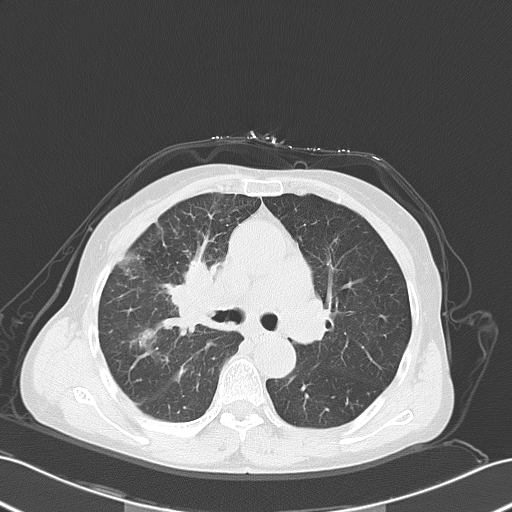
Chest CT, one axial slice; position 34 of 55 along the scan axis; 120 kVp; lung window (W 1500 / L -600 HU); 5 mm slice thickness; 512 × 512 image matrix, field of view 353 × 353 mm. Patient: female, 67 years. From the clinical record (not read from this slice): clinical TNM (as recorded): T2a N3 M0.
Outlined on this slice (rectangle marked by the reading radiologist):
- lung tumour (recorded histology: small cell carcinoma): bounding box <167,250,224,330> (left, top, right, bottom; pixels)